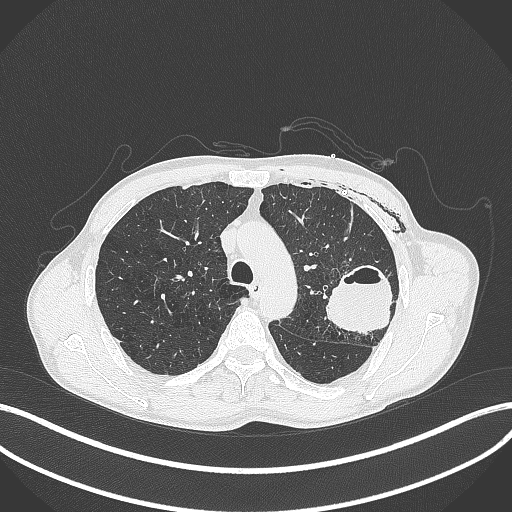
Chest CT, one axial slice; slice 292 of 457 in the series (ordered by position); reconstruction kernel B70f; lung window (W 1500 / L -600 HU); 1 mm slice thickness; 512 × 512 image matrix, field of view 400 × 400 mm. Male patient, age 58 years. From the clinical record (not read from this slice): clinical TNM (as recorded): T3 N0 M0.
Annotated regions visible in this slice (bounding box drawn by a radiologist):
- lung tumour (recorded histology: adenocarcinoma): bounding box <327,261,400,337> (left, top, right, bottom; pixels)